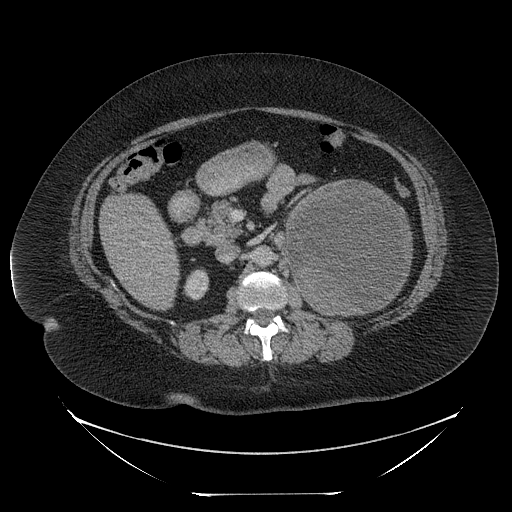
Contrast-enhanced abdominal CT, one axial slice. Position 130 of 205 along the scan axis. Intravenous contrast given. Soft-tissue window (W 400 / L 40 HU). 2.5 mm slice thickness. 512 × 512 image matrix, field of view 500 × 500 mm. Patient: female, 53 years. From the clinical record (not read from this slice): diagnosis: adrenocortical carcinoma; tumour side: left adrenal; tumour size at pathology: 17 cm; Ki-67 index: 20 %; stage (as recorded): 3.
Outlined on this slice (semi-automatically segmented with operator editing):
- mass: bounding box (x1, y1, x2, y2) in pixels: (288, 182, 411, 314)